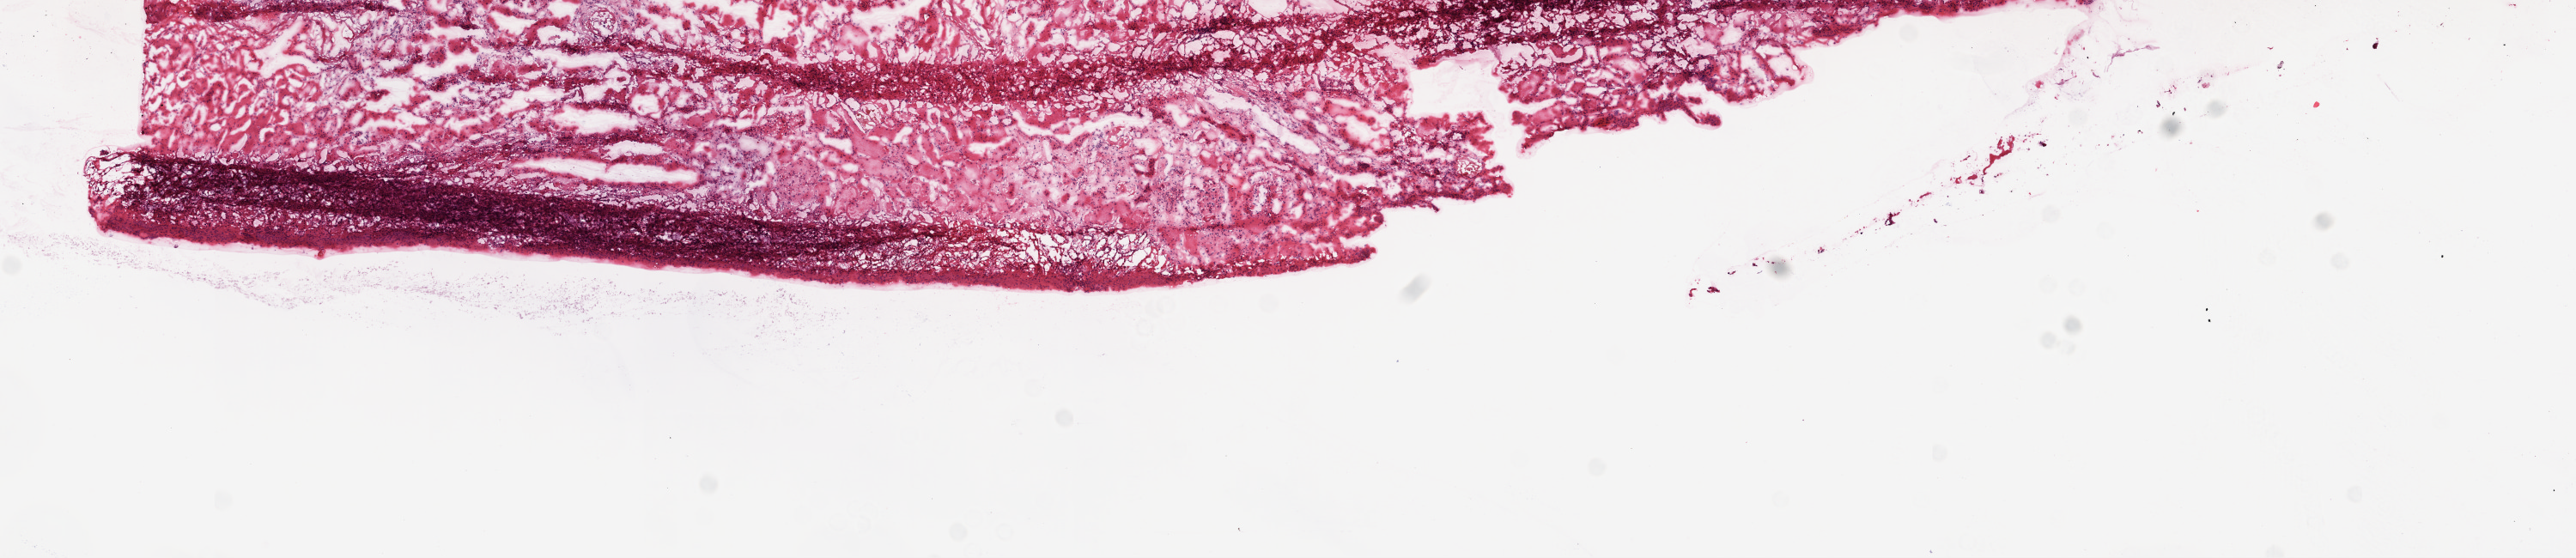
H&E whole-slide image, low-resolution overview of the scanned area, about 12.0 x 2.6 mm; frozen section from the top of the tissue portion; kidney, solid tissue normal (non-tumour tissue) sample. Male patient; age at initial diagnosis 63 years.
* this section: solid tissue normal (non-tumour) sample from the same patient
* patient diagnosis: Clear cell adenocarcinoma, NOS